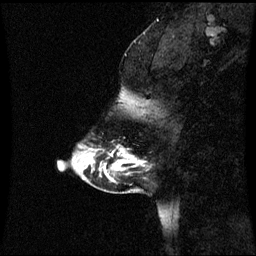
Breast MRI (dynamic contrast-enhanced), one sagittal slice. Slice 13 of 60 in the series (ordered by position). Dynamic contrast-enhanced series, image 2 of 3 at this slice position (ordered by acquisition). 1.5 T. TE 4.2 ms, TR 8.9 ms. 2 mm slice thickness. 256 × 256 image matrix, field of view 220 × 220 mm. Patient: female, 43 years. Case-level facts recorded for this patient, not image findings: setting: breast cancer imaged before/during neoadjuvant chemotherapy; receptor status: HR-positive, HER2-negative.
Annotated regions visible in this slice (semi-automatic segmentation, software-assisted and operator-edited):
- analysis volume of interest (the breast-tissue region the enhancement analysis was run in; not a lesion): box from (x=84, y=116) to (x=144, y=171) px
- tumour enhancement mask (voxels above the 70 % enhancement threshold inside the analysis volume of interest): (x=104, y=150)–(x=124, y=171)